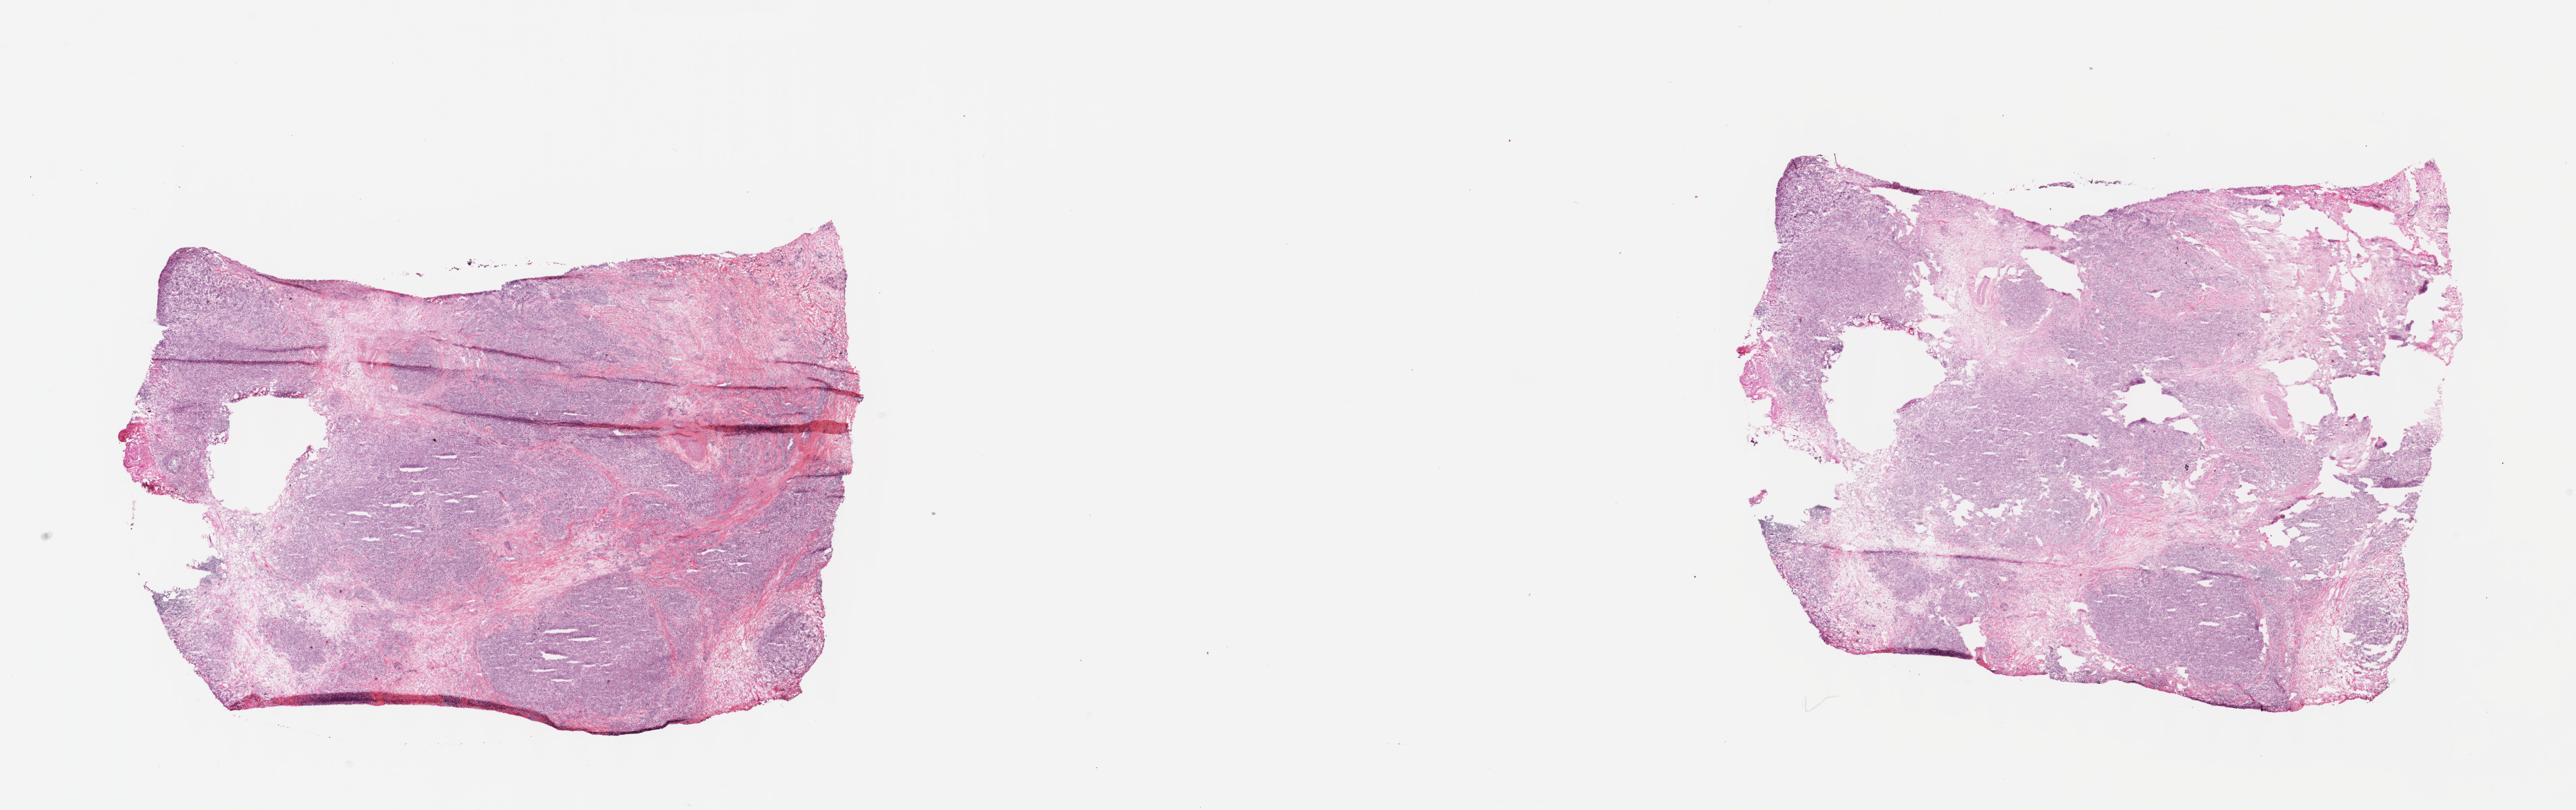
H&E-stained whole-slide image, shown as a low-resolution overview of the whole scanned area (about 30.2 x 9.5 mm, acquisition: 40x scan); FFPE section; sample: primary tumour, breast. Female, age 66 years at initial diagnosis.
AJCC pathologic stage: IIA. TNM: T2 N0 M0. Histologic diagnosis: Infiltrating duct carcinoma, NOS.